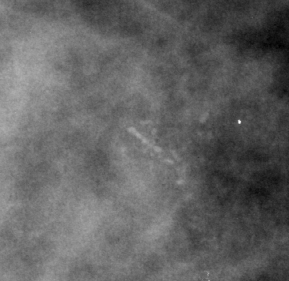
Crop from a digitized film mammogram around one marked abnormality; right breast; MLO view.
- Calcifications, morphology pleomorphic, distribution clustered; BI-RADS assessment category 4; pathology result (as recorded, not read from the image): malignant.